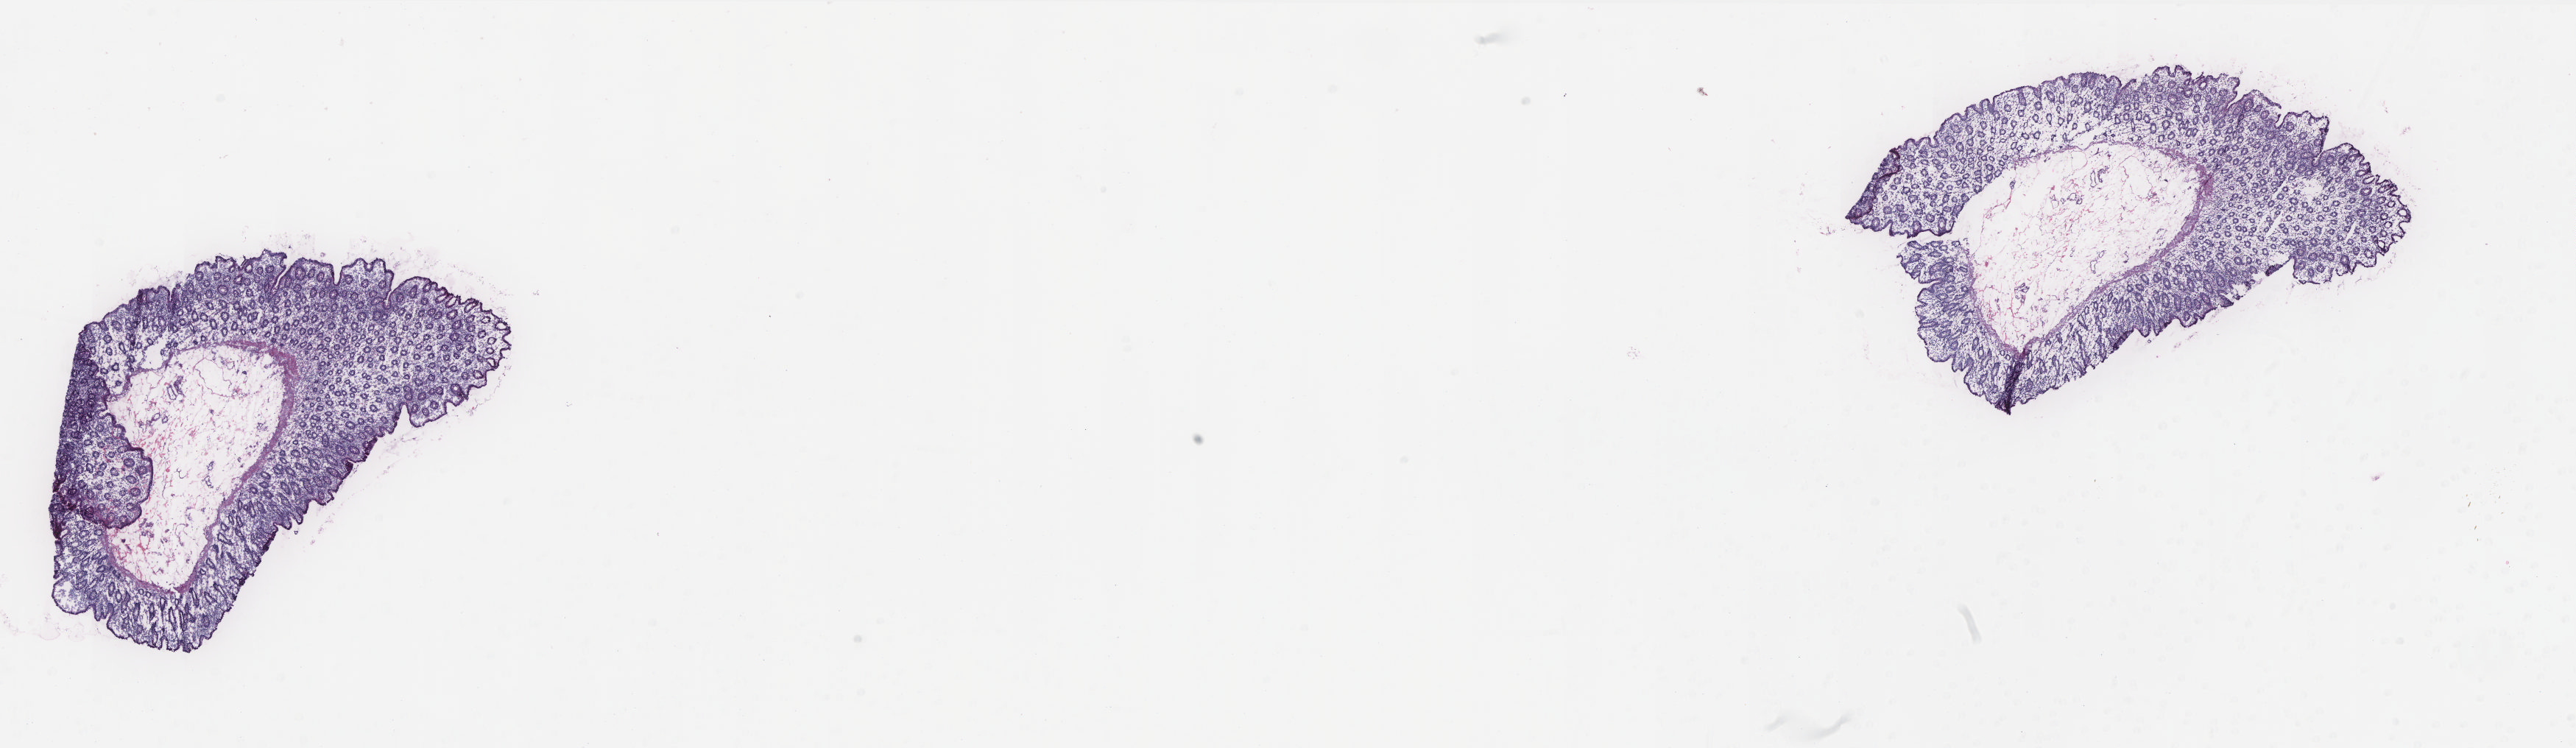
H&E-stained whole-slide image, a low-resolution overview of the entire scanned area, about 27.9 x 8.1 mm. Frozen section from the bottom of the tissue portion. Solid tissue normal (non-tumour tissue) sample from the colon. Male patient; age at initial diagnosis 82 years. Composition of this section per pathologist review: tumour cells 0%, normal cells 100%. Infiltration values recorded for this section: lymphocyte infiltration 35%, monocyte infiltration 10%, neutrophil infiltration 0%.
This section: solid tissue normal sample (biorepository sample class). Patient diagnosis: Adenocarcinoma, NOS (transverse colon).